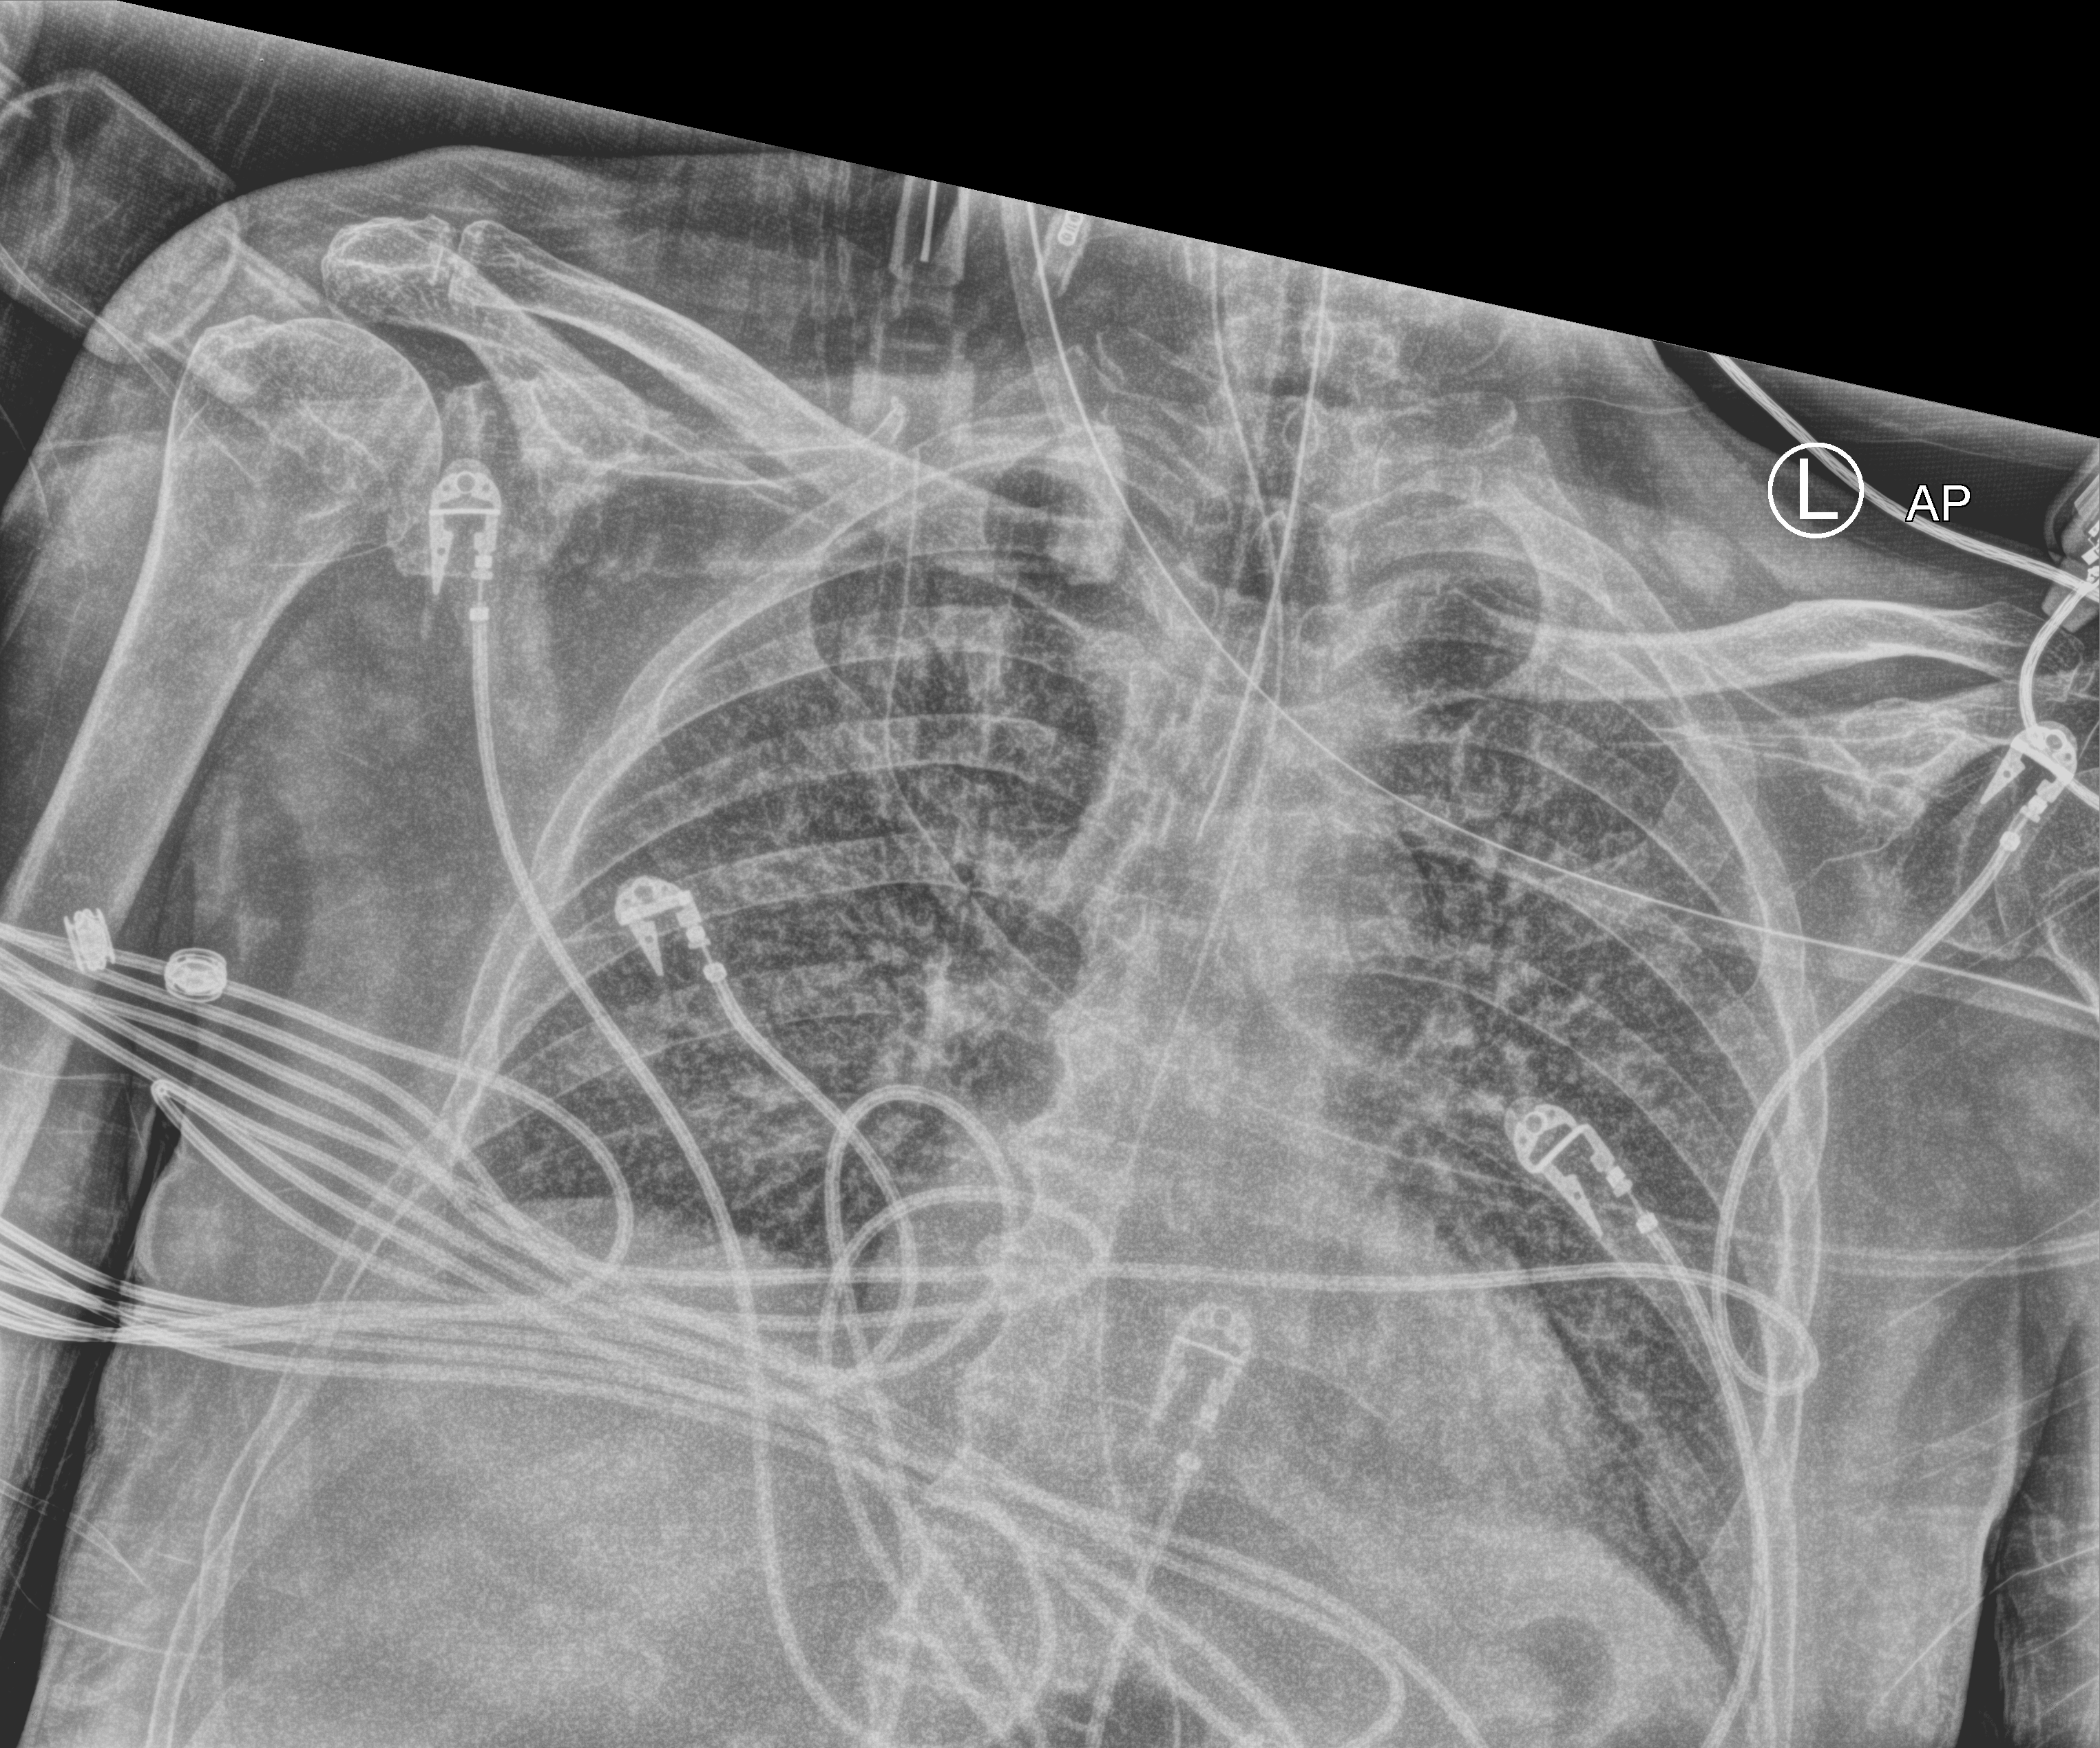
Chest X-ray (portable). Patient hospitalised with COVID-19; male, aged 75–90 years.
Admission-level facts for this patient (not findings on this image; timing relative to this image not recorded): admitted to intensive care during this hospital stay: yes; COPD (admission record): no.